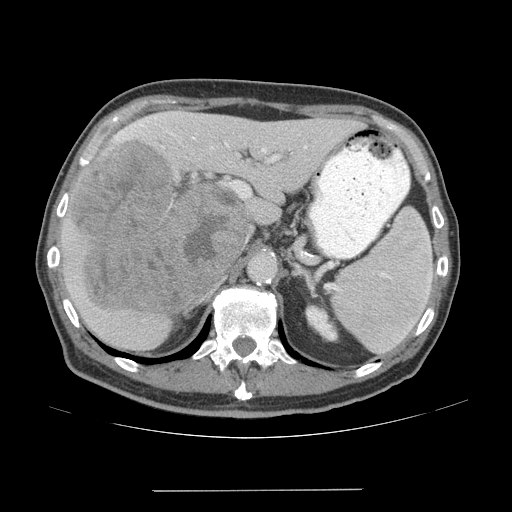
Contrast-enhanced abdominal CT (liver protocol), one axial slice; slice 39 of 77 in the series (ordered by position); 140 kVp; soft-tissue window (W 400 / L 40 HU); 2.5 mm slice thickness; 512 × 512 image matrix, field of view 400 × 400 mm. From the clinical record (not read from this slice): diagnosis: hepatocellular carcinoma (patient treated with transarterial chemoembolisation; whether this scan precedes or follows treatment is not stated here); TNM stage (as recorded): Stage-IVA; Child-Pugh class: A; tumour differentiation: well differentiated; tumour nodularity: uninodular.
Structures marked on this image (semi-automatic segmentation, software-assisted and operator-edited):
- liver parenchyma outside the tumour (the mass and vessels are separate outlines, so this box may not span the whole liver): bounding box (x1, y1, x2, y2) in pixels: (60, 110, 363, 350)
- mass: (69, 140, 250, 315)
- liver vessels: (114, 116, 307, 161)